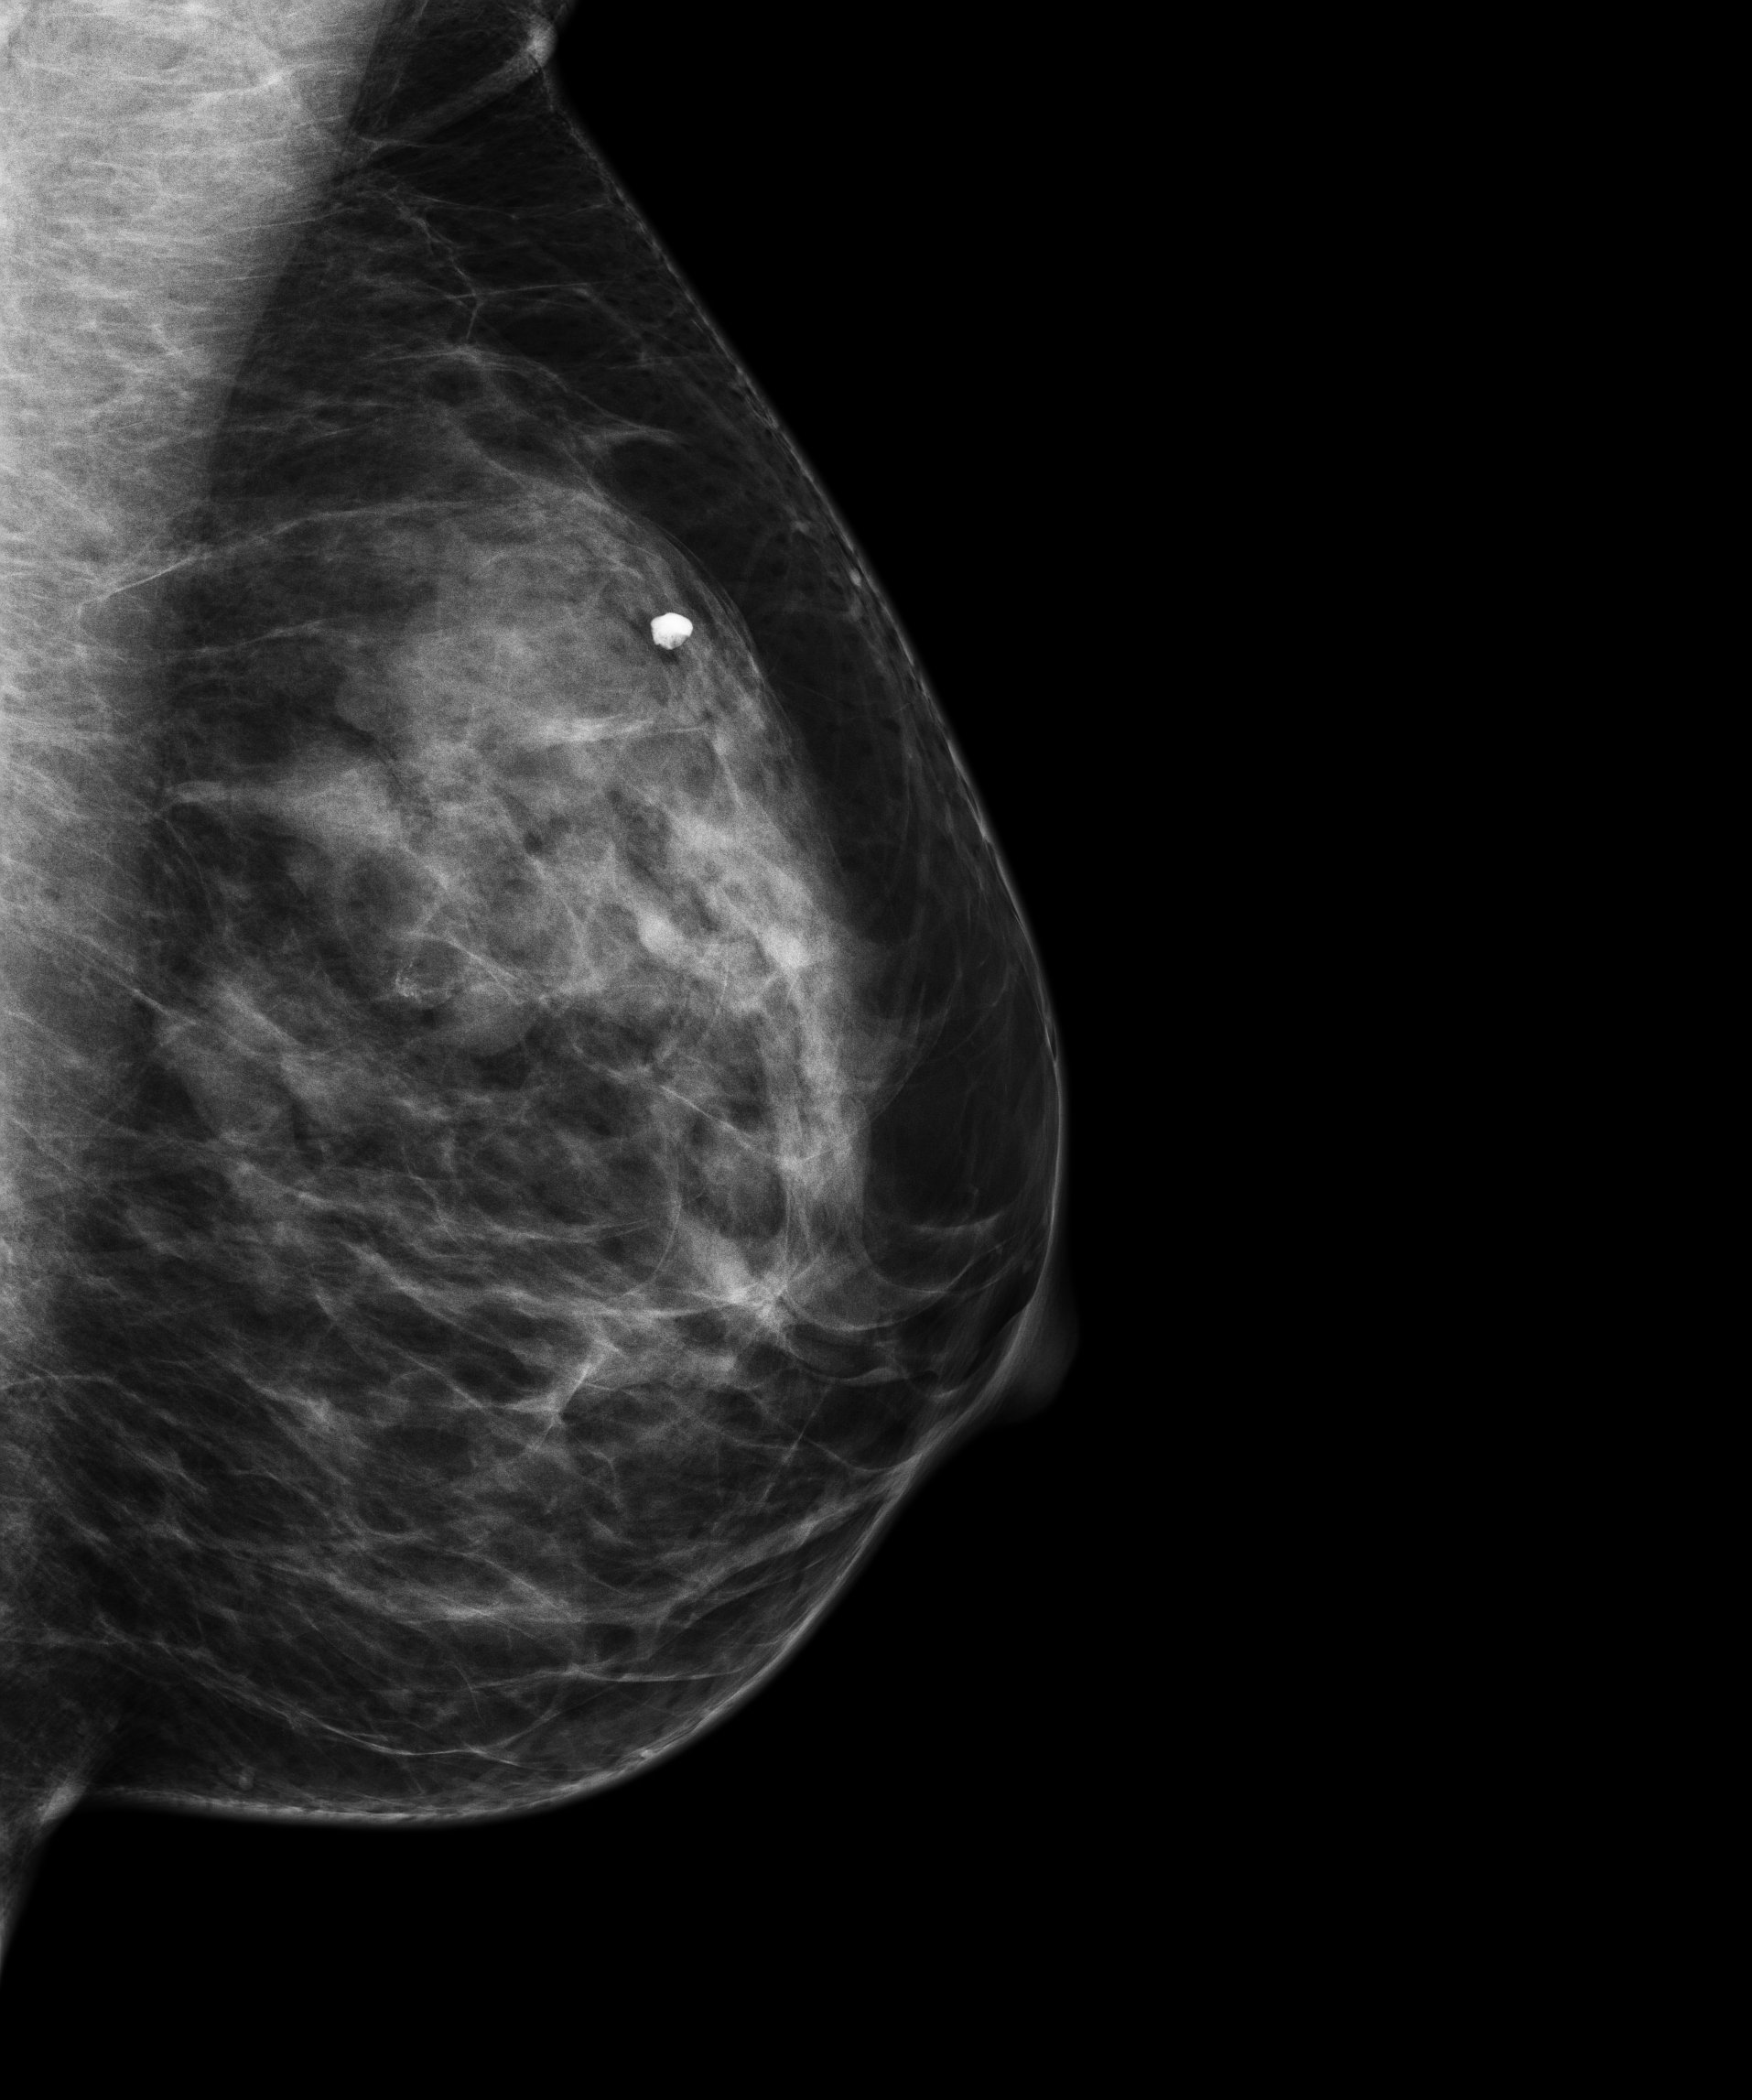
Digital mammogram (FFDM), left breast, MLO view, annual screening mammography examination, compressed breast thickness 55 mm. Female patient, age 51 years.
Breast density at the screening exam (both breasts): heterogeneously dense (BI-RADS density category c).